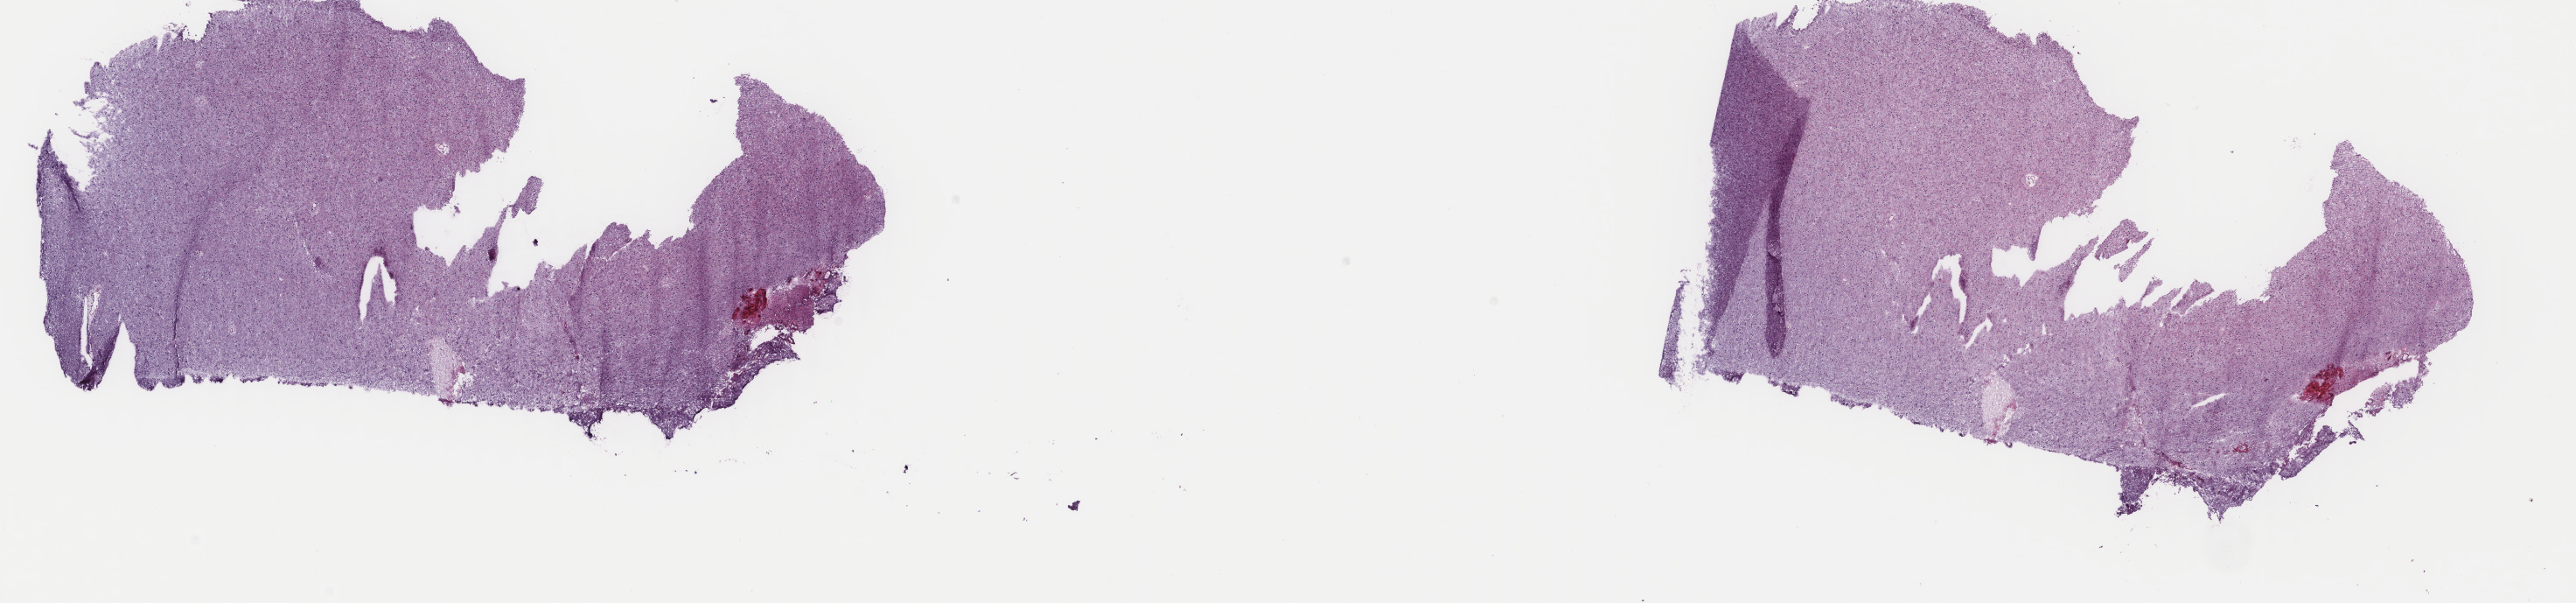
Hematoxylin and eosin (H&E) stained whole-slide image — low-resolution overview of the scanned area, about 23.4 x 5.5 mm, frozen section from the top of the tissue portion, primary tumour sample from the brain. Patient: female, age at initial diagnosis 23 years. Histologic grade: G2 (moderately differentiated). Composition of this section per pathologist review: tumour cells 50%, tumour nuclei 80%, normal cells 10%, stromal cells 40%, necrosis 0%. Inflammatory infiltration, as recorded: lymphocyte infiltration 0%, monocyte infiltration 0%, neutrophil infiltration 0%.
Histologic diagnosis: Mixed glioma (cerebrum).